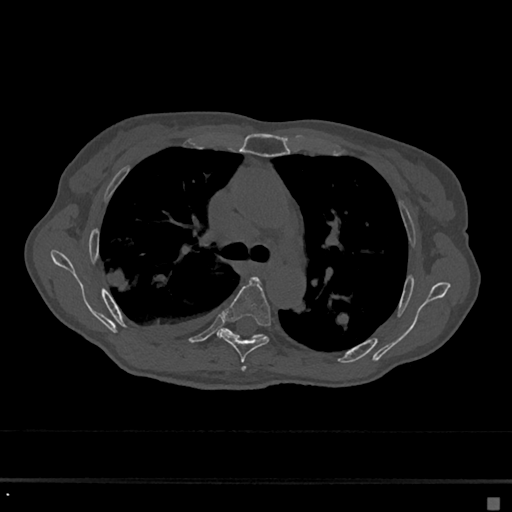
CT including the spine, one axial slice. Position 454 of 797 along the scan axis. Bone window (W 1800 / L 400 HU). 0.5 mm slice thickness. 512 × 512 image matrix, field of view 360 × 360 mm. Patient: female, 68 years. From the clinical record (not read from this slice): primary cancer: renal.
Outlined on this slice (semi-automatically segmented with operator editing):
- T4 vertebra: bounding box [x1, y1, x2, y2] px = [242, 367, 246, 371]
- T5 vertebra: [218, 278, 271, 363]
- T6 vertebra: [217, 328, 266, 339]